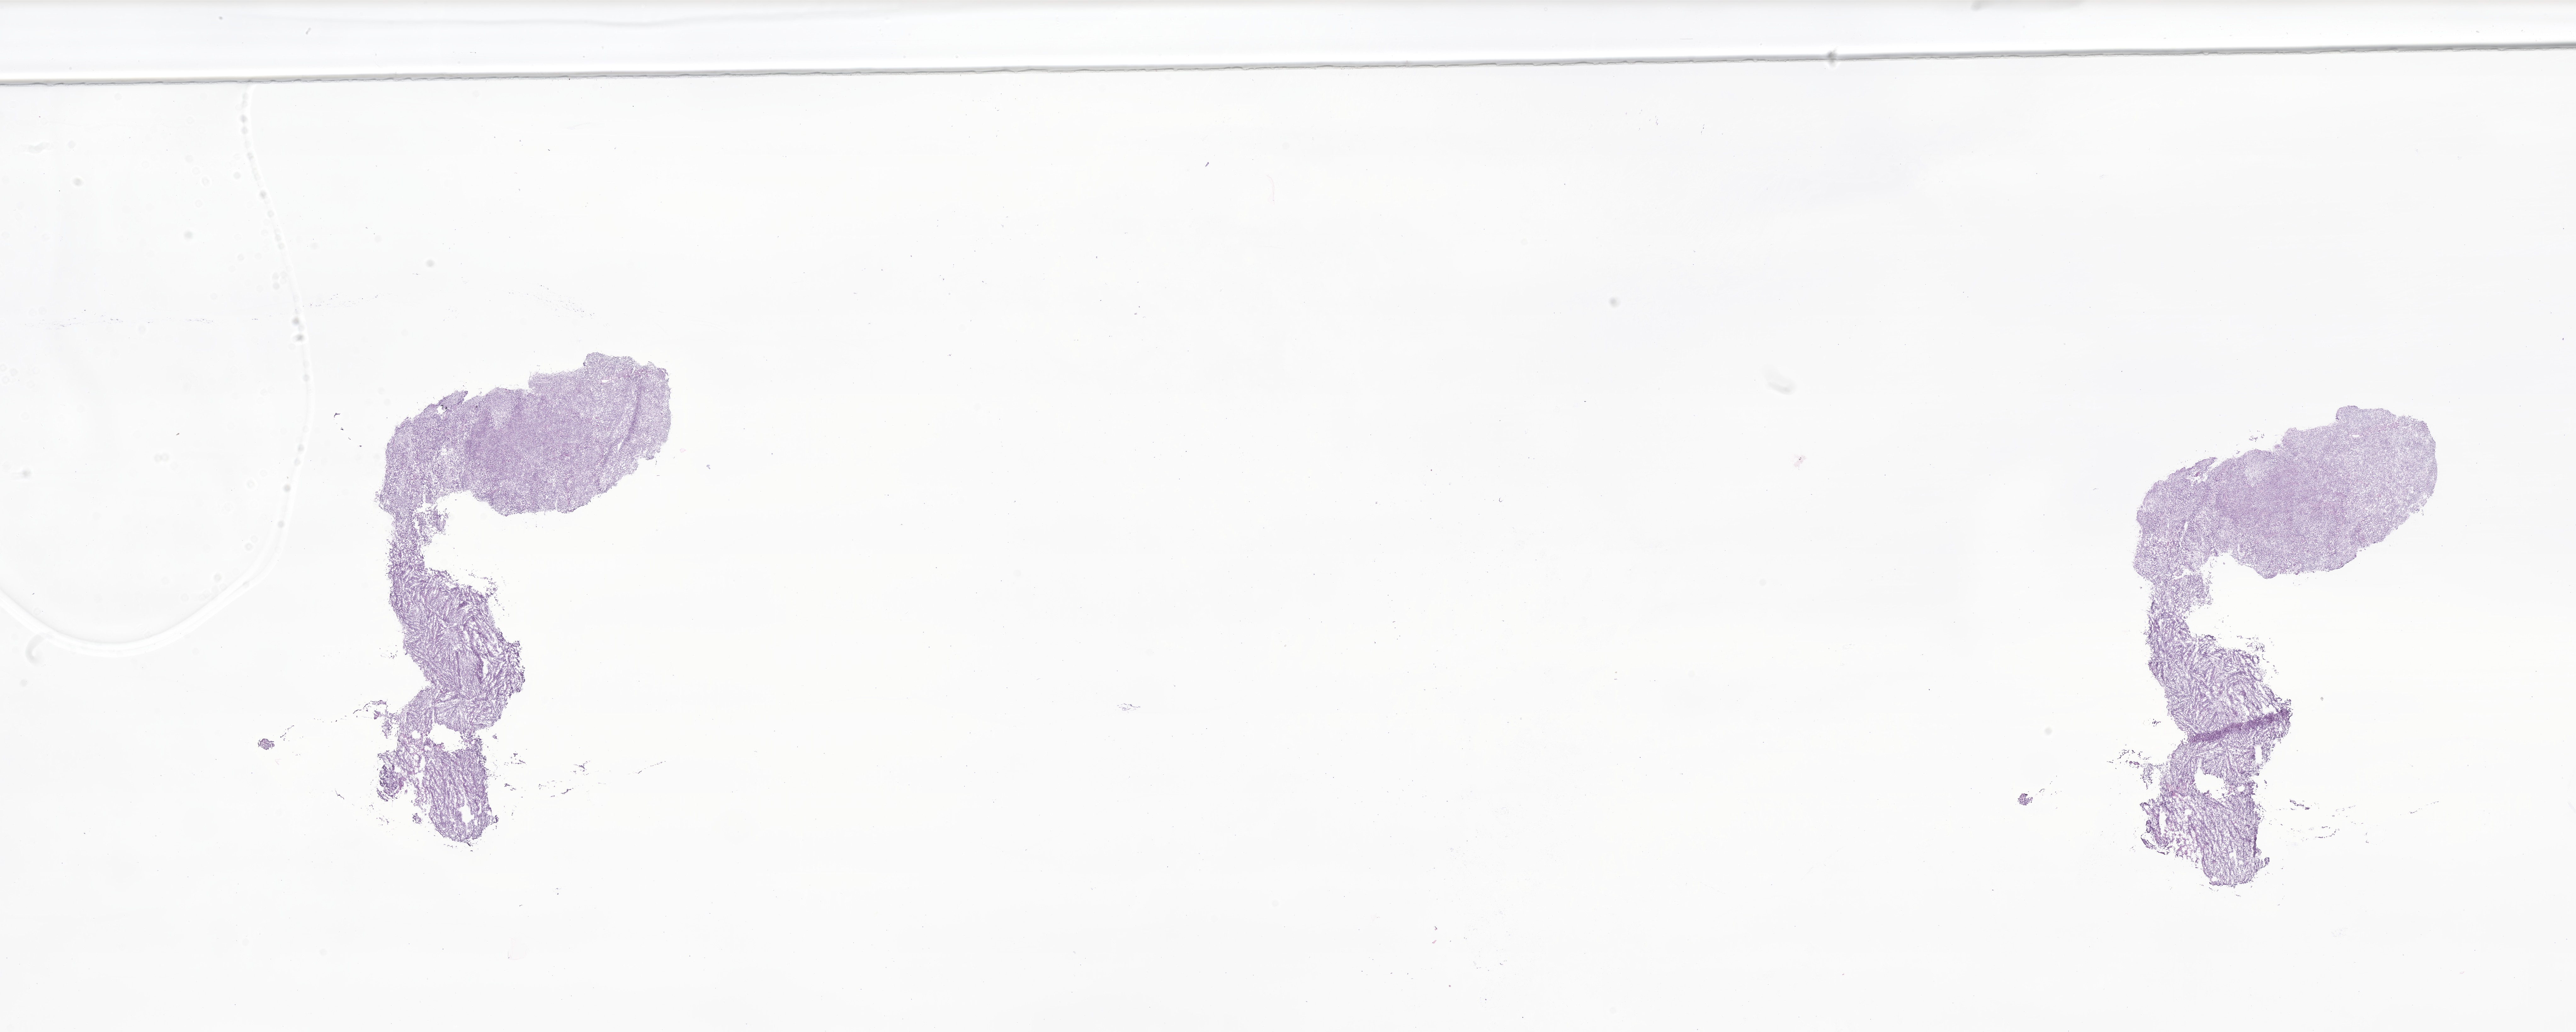
Digitized hematoxylin and eosin (H&E)-stained section of tumor tissue from the cerebellum — shown as a low-resolution overview of the whole scanned area (about 34.5 x 13.8 mm). Frozen section (OCT-embedded). Patient: female, age 378 days.
Recorded diagnosis: Medulloblastoma, NOS.